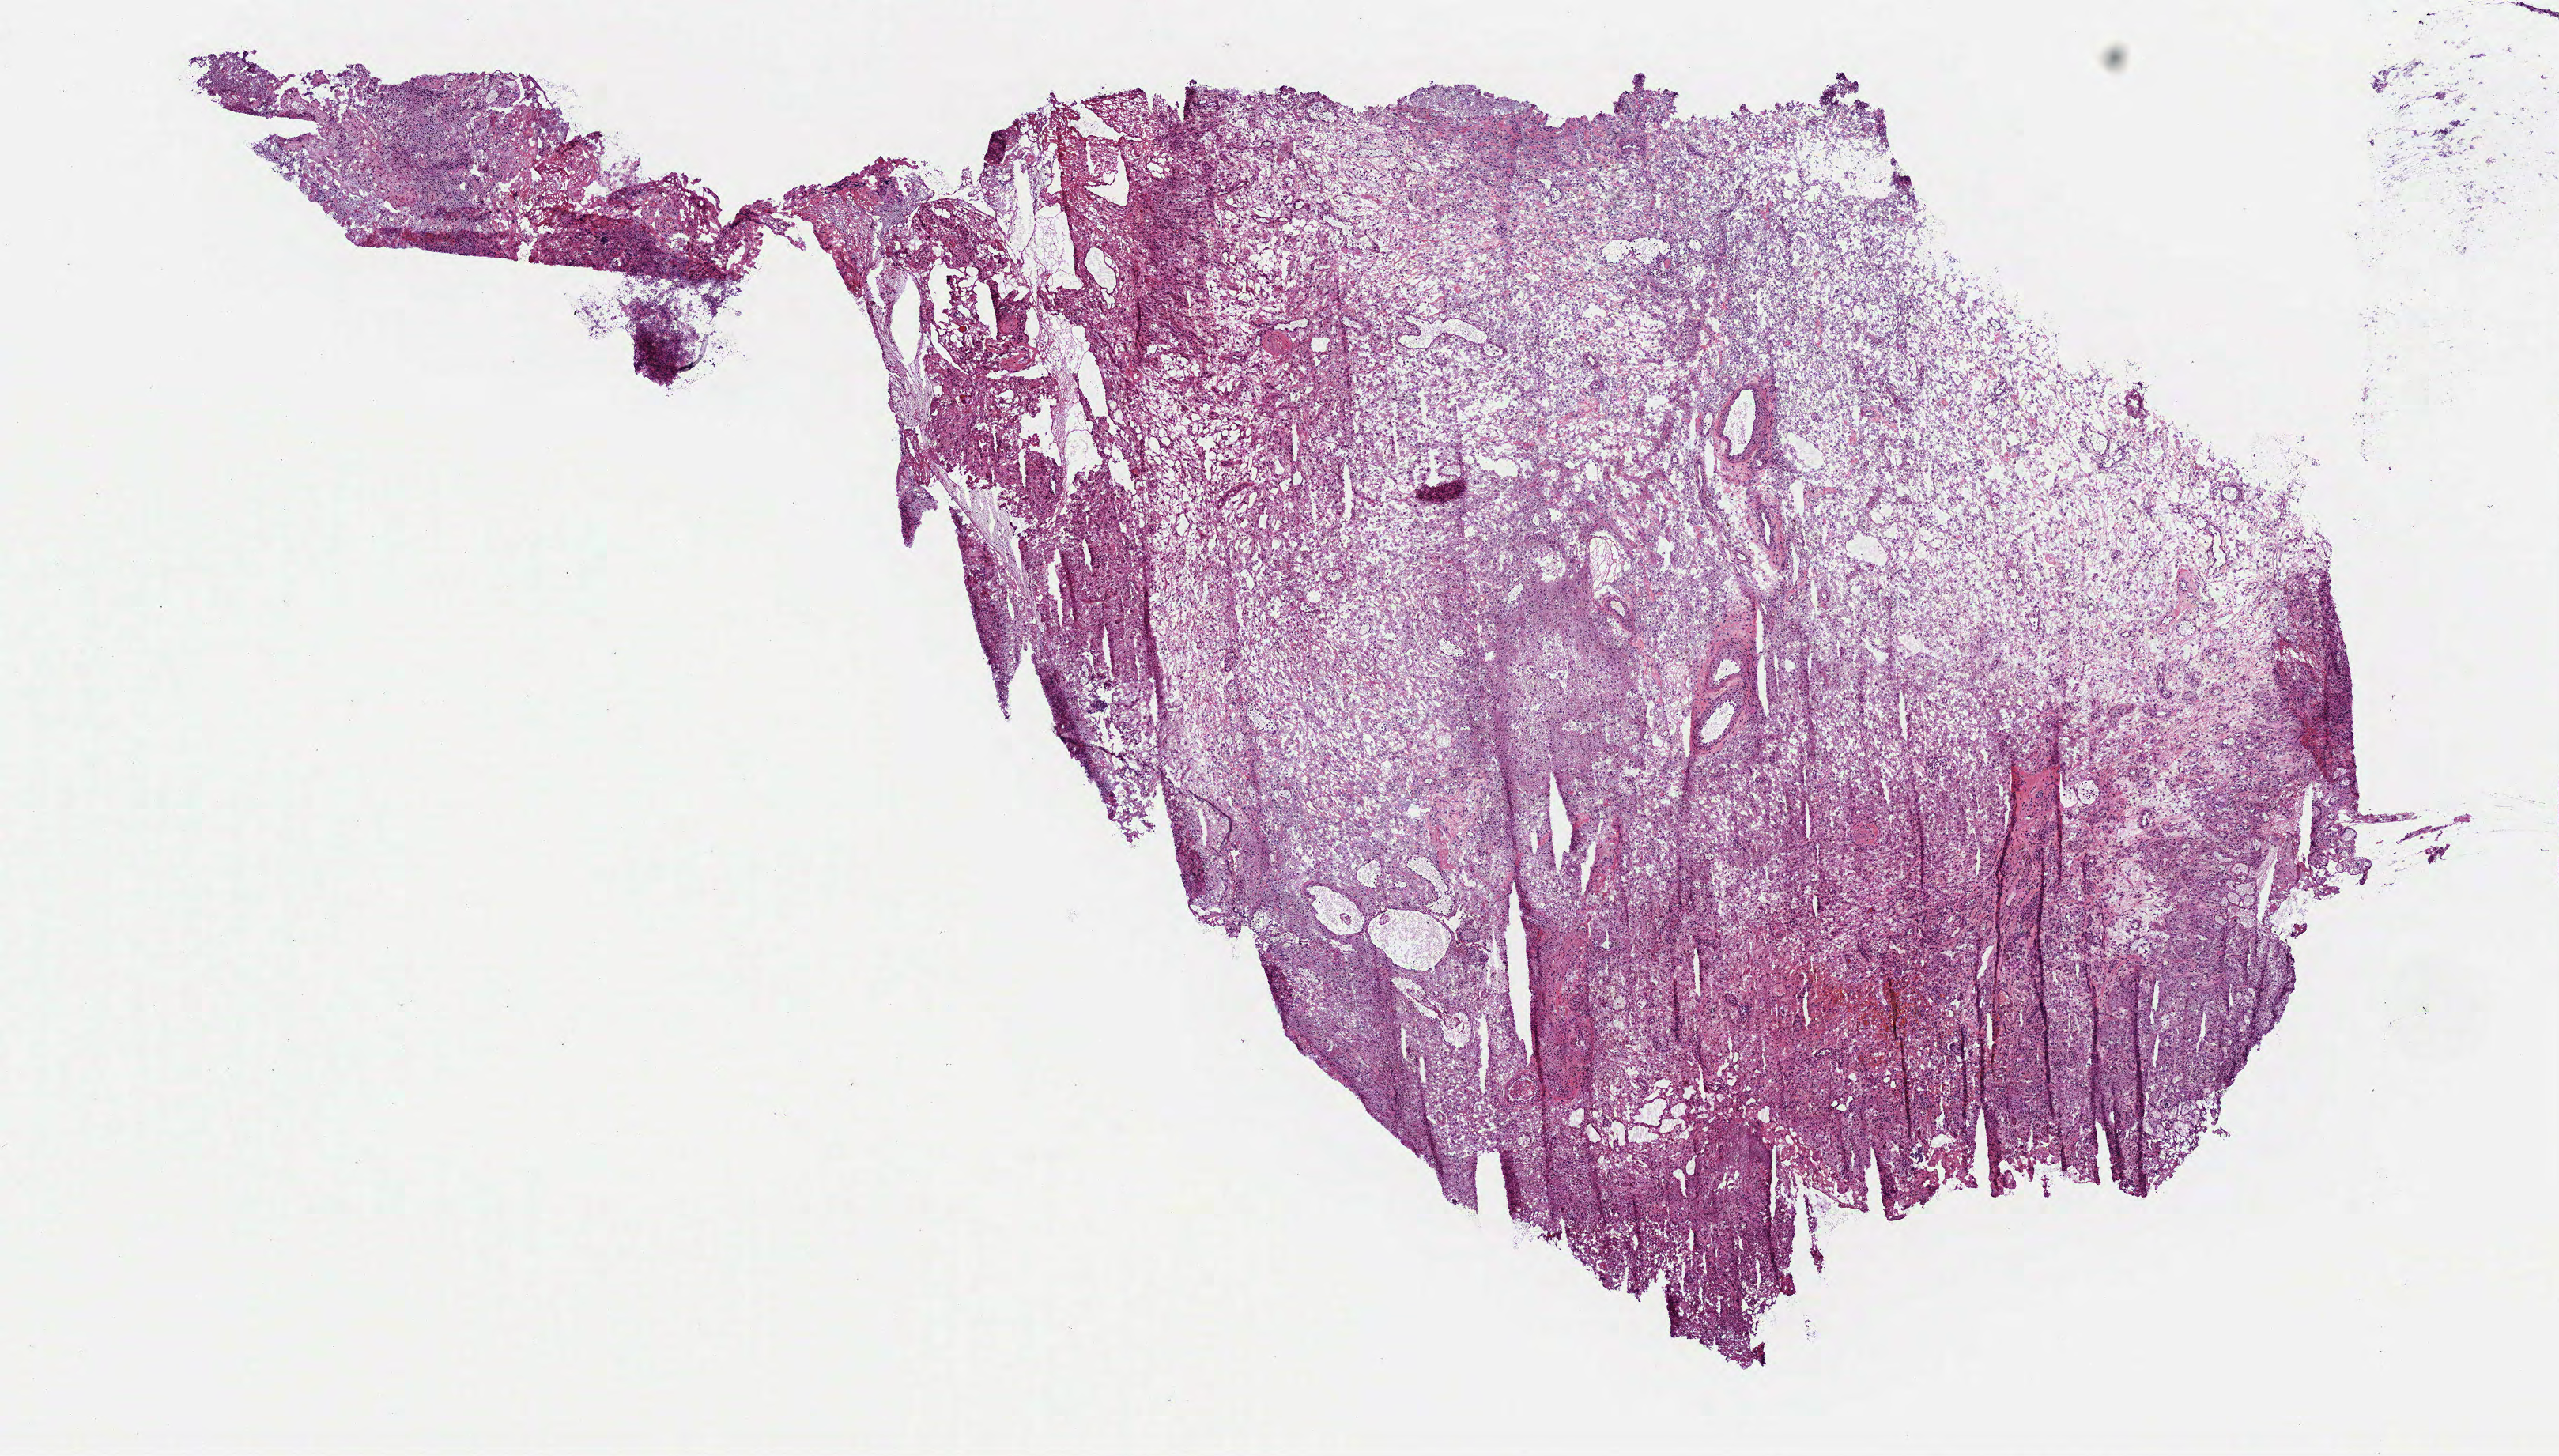
Digitized H&E-stained tissue section (whole slide), whole scanned area (about 13.1 x 7.4 mm) shown as a low-resolution overview, frozen section from the top of the tissue portion, sample: primary tumour, brain. Patient: male, age at initial diagnosis 66 years. Slide review estimates, as recorded: tumour cells 88%, tumour nuclei 85%.
Diagnosis: Oligodendroglioma, anaplastic (cerebrum).